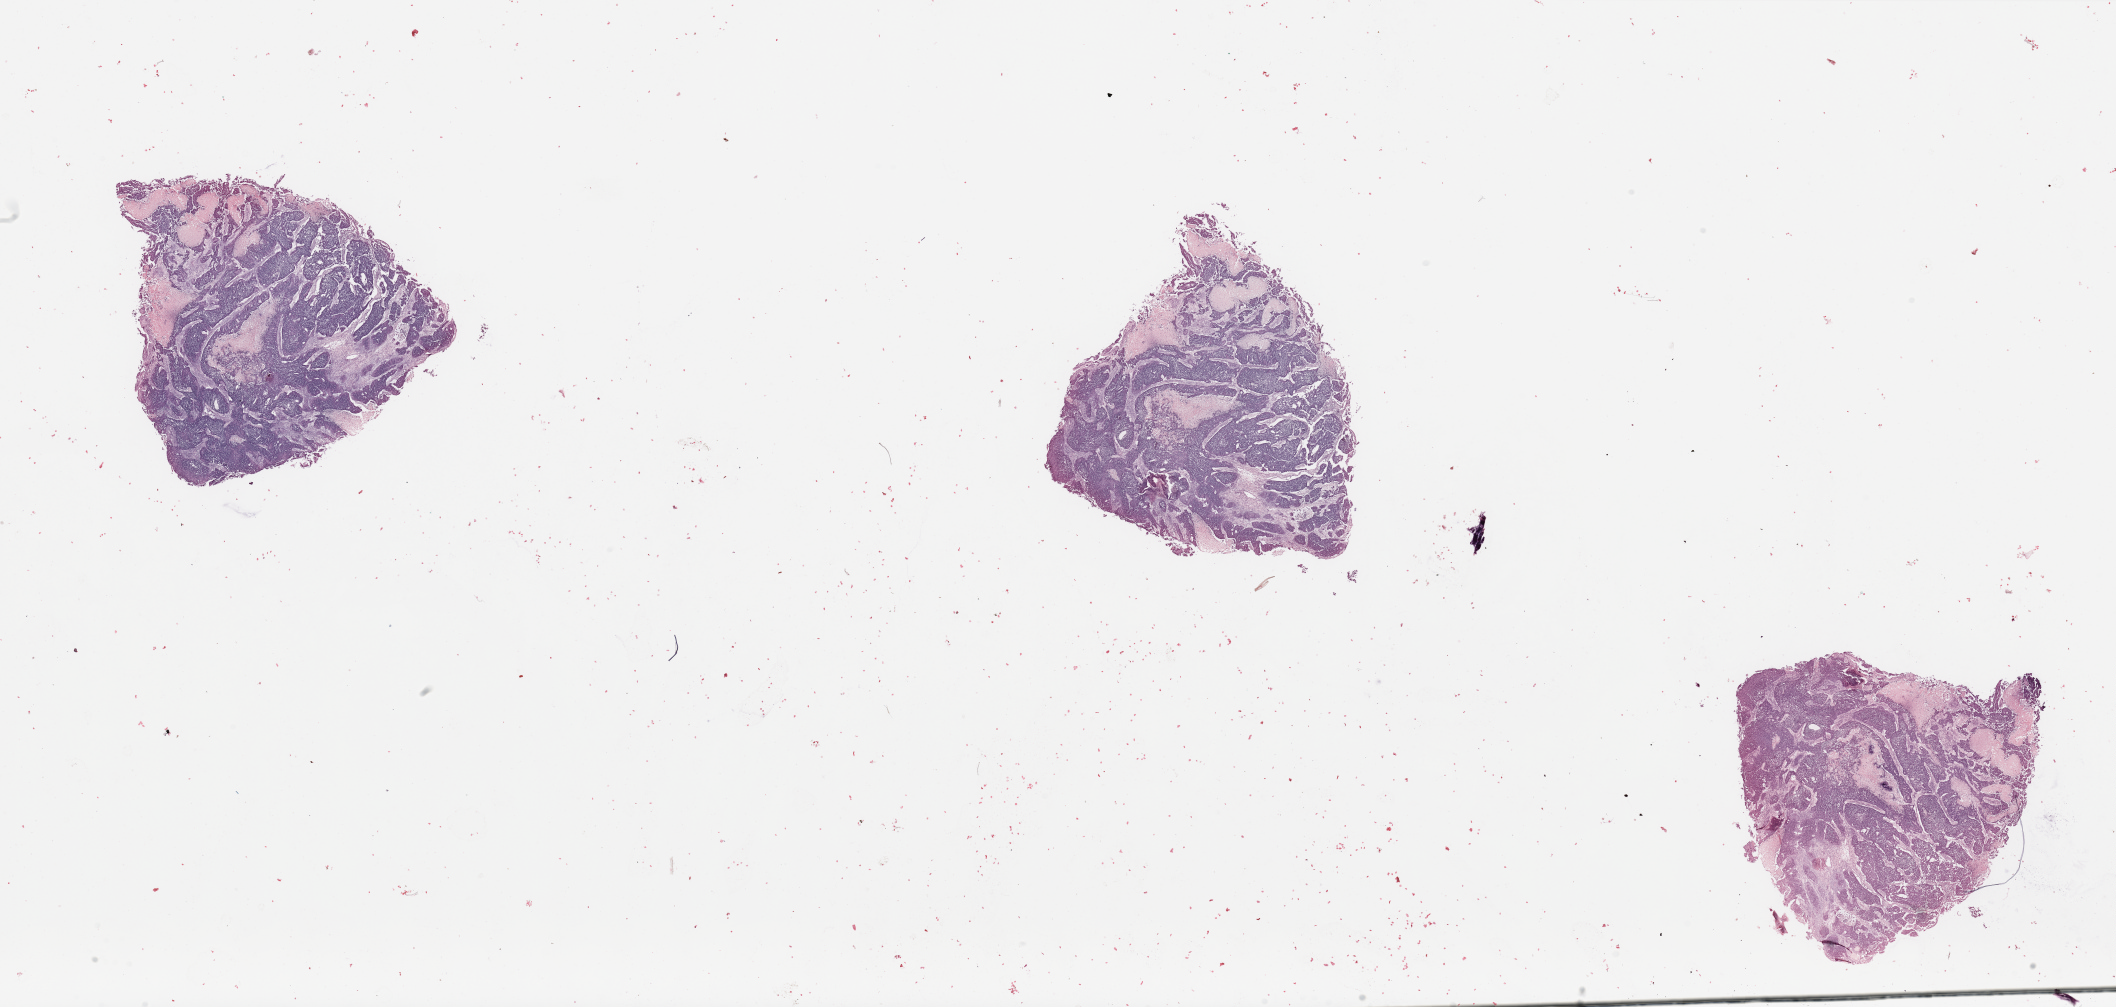
Whole-slide histology image, Hematoxylin and eosin (H&E) stained — low-resolution overview of the scanned area, about 33.5 x 15.9 mm (acquisition: 20x scan), tumour tissue sample, sampled site: uterus. Patient: female, age 61 years. Histologic grade: G3 (poorly differentiated). Pathologist review of this section (percent, as recorded): tumour nuclei 90%, necrosis 10%.
• primary tumour site (as recorded): posterior endometrium
• histologic diagnosis: Endometrioid adenocarcinoma, NOS
• AJCC pathologic stage: I